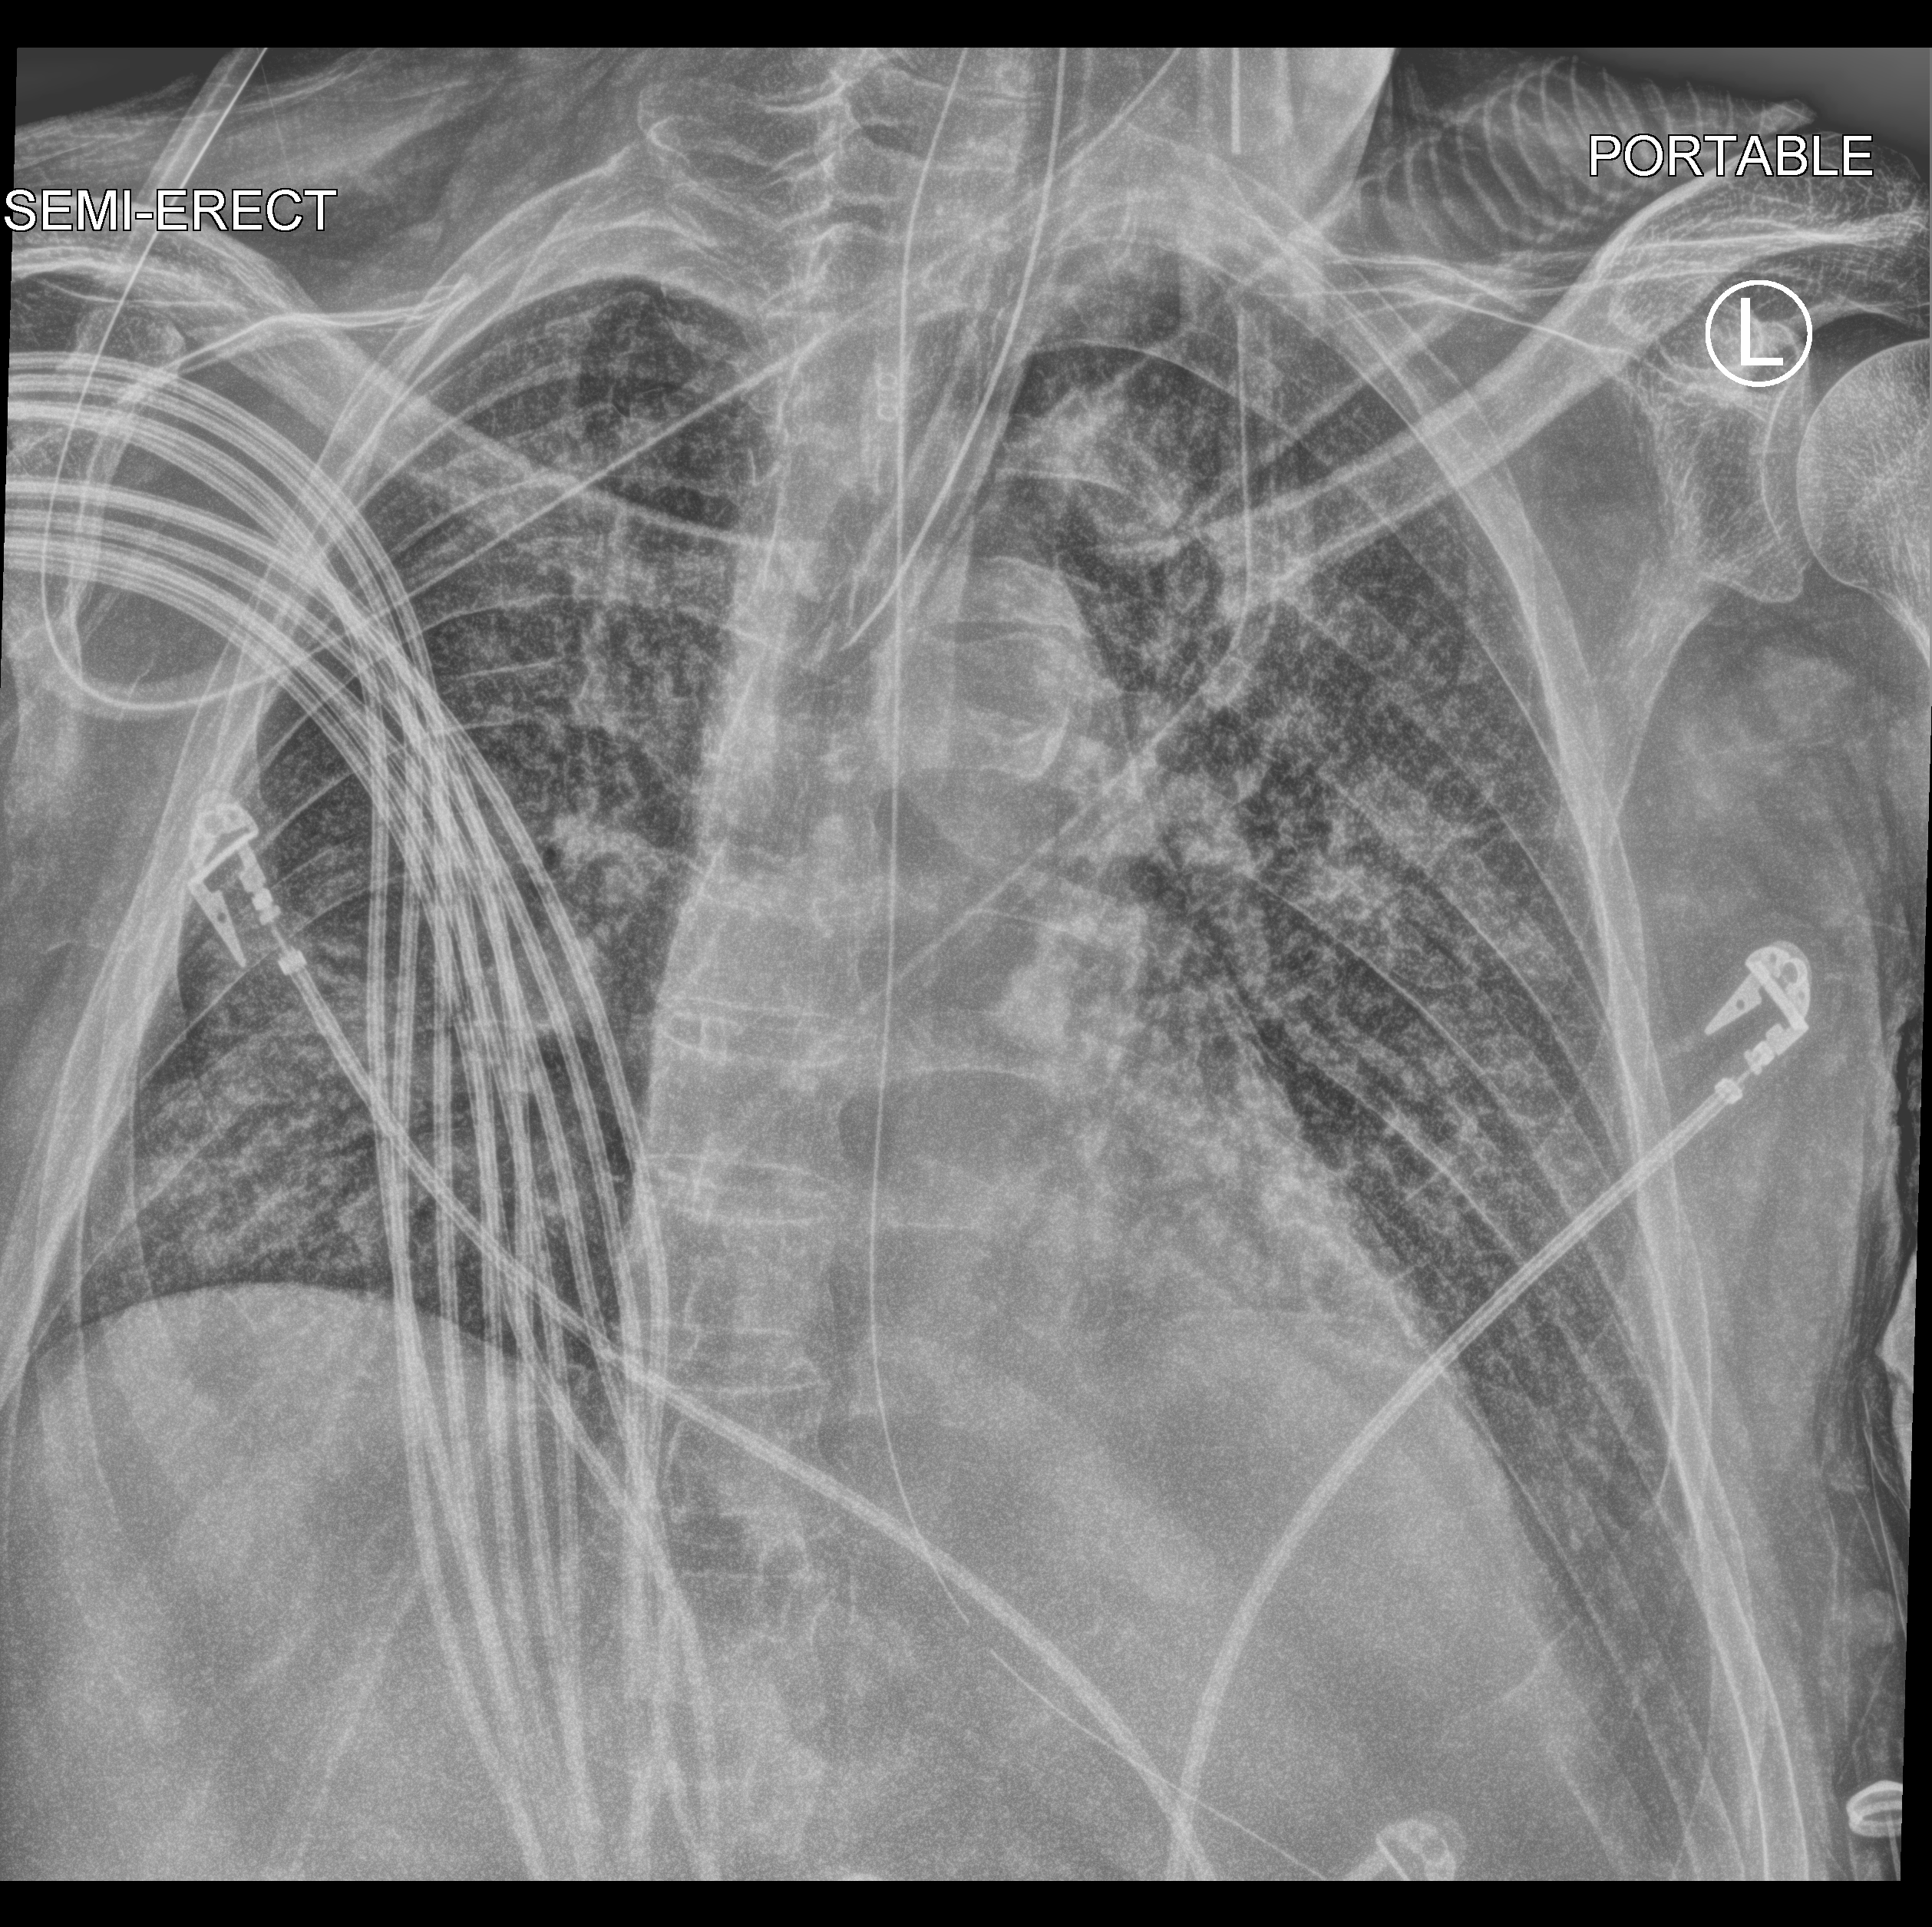
Bedside chest radiograph (computed radiography); anteroposterior (AP) projection. Male patient hospitalised with COVID-19, age 60–74 years.
Hospital-stay facts (about this admission, not read from this image; timing relative to this image not recorded): chronic kidney disease (admission record): no; admitted to intensive care during this hospital stay: yes; mechanically ventilated during this hospital stay: yes.